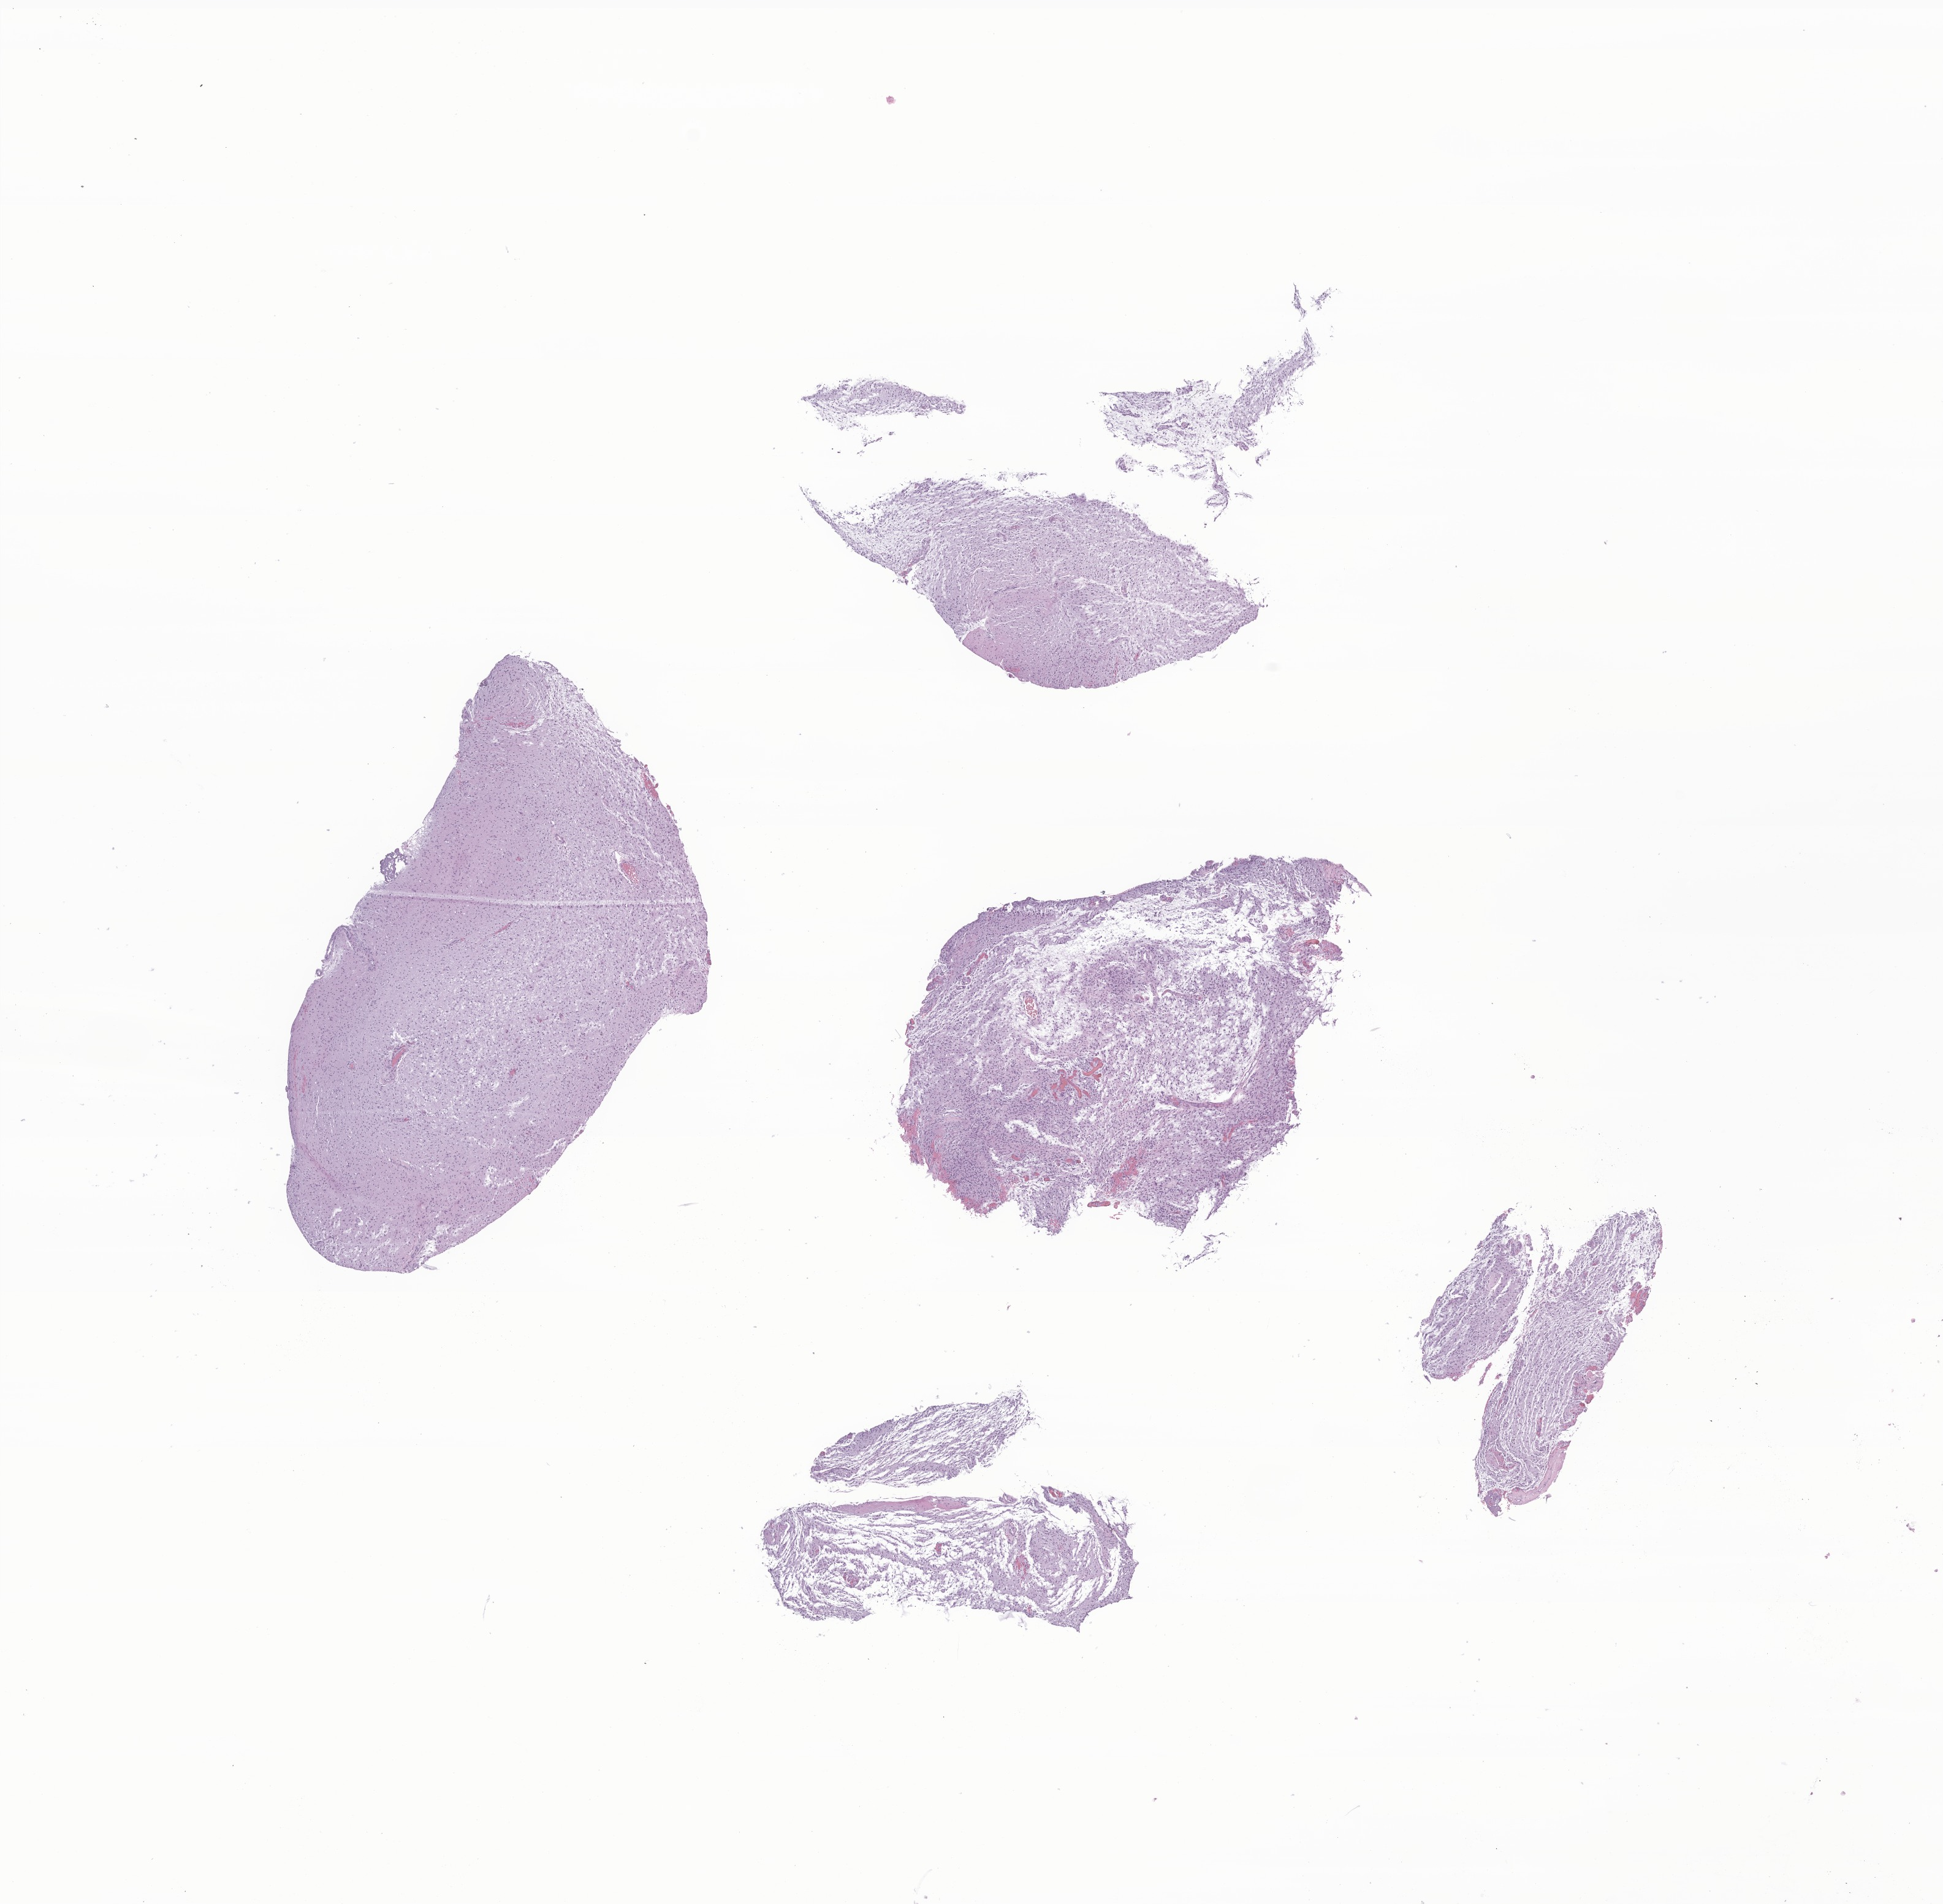
Whole-slide image, hematoxylin and eosin (H&E) stain of tumor tissue from the spinal cord — whole scanned area (about 13.4 x 13.1 mm) shown as a low-resolution overview; formalin-fixed paraffin-embedded section. Female patient, age 711 days (about 1.9 years).
Diagnosis (ICD-O-3 morphology term): Glioma, malignant.